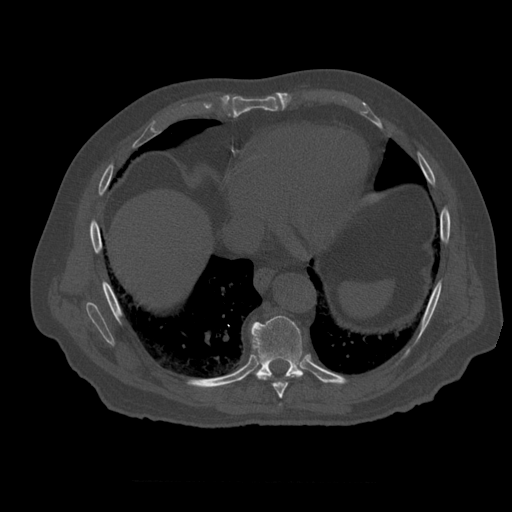
CT including the spine, one axial slice; position 329 of 399 along the scan axis; reconstruction kernel STANDARD; 120 kVp; bone window (W 1800 / L 400 HU); 1.25 mm slice thickness; 512 × 512 image matrix, field of view 407 × 407 mm. Patient age 73 years. Case-level facts recorded for this patient, not image findings: primary cancer: prostate; vertebrae with lytic lesions (as recorded): L2.
Outlined on this slice (semi-automatically segmented with operator editing):
- T8 vertebra: box from (x=259, y=374) to (x=300, y=399) px
- T9 vertebra: (x=252, y=316)–(x=304, y=378)